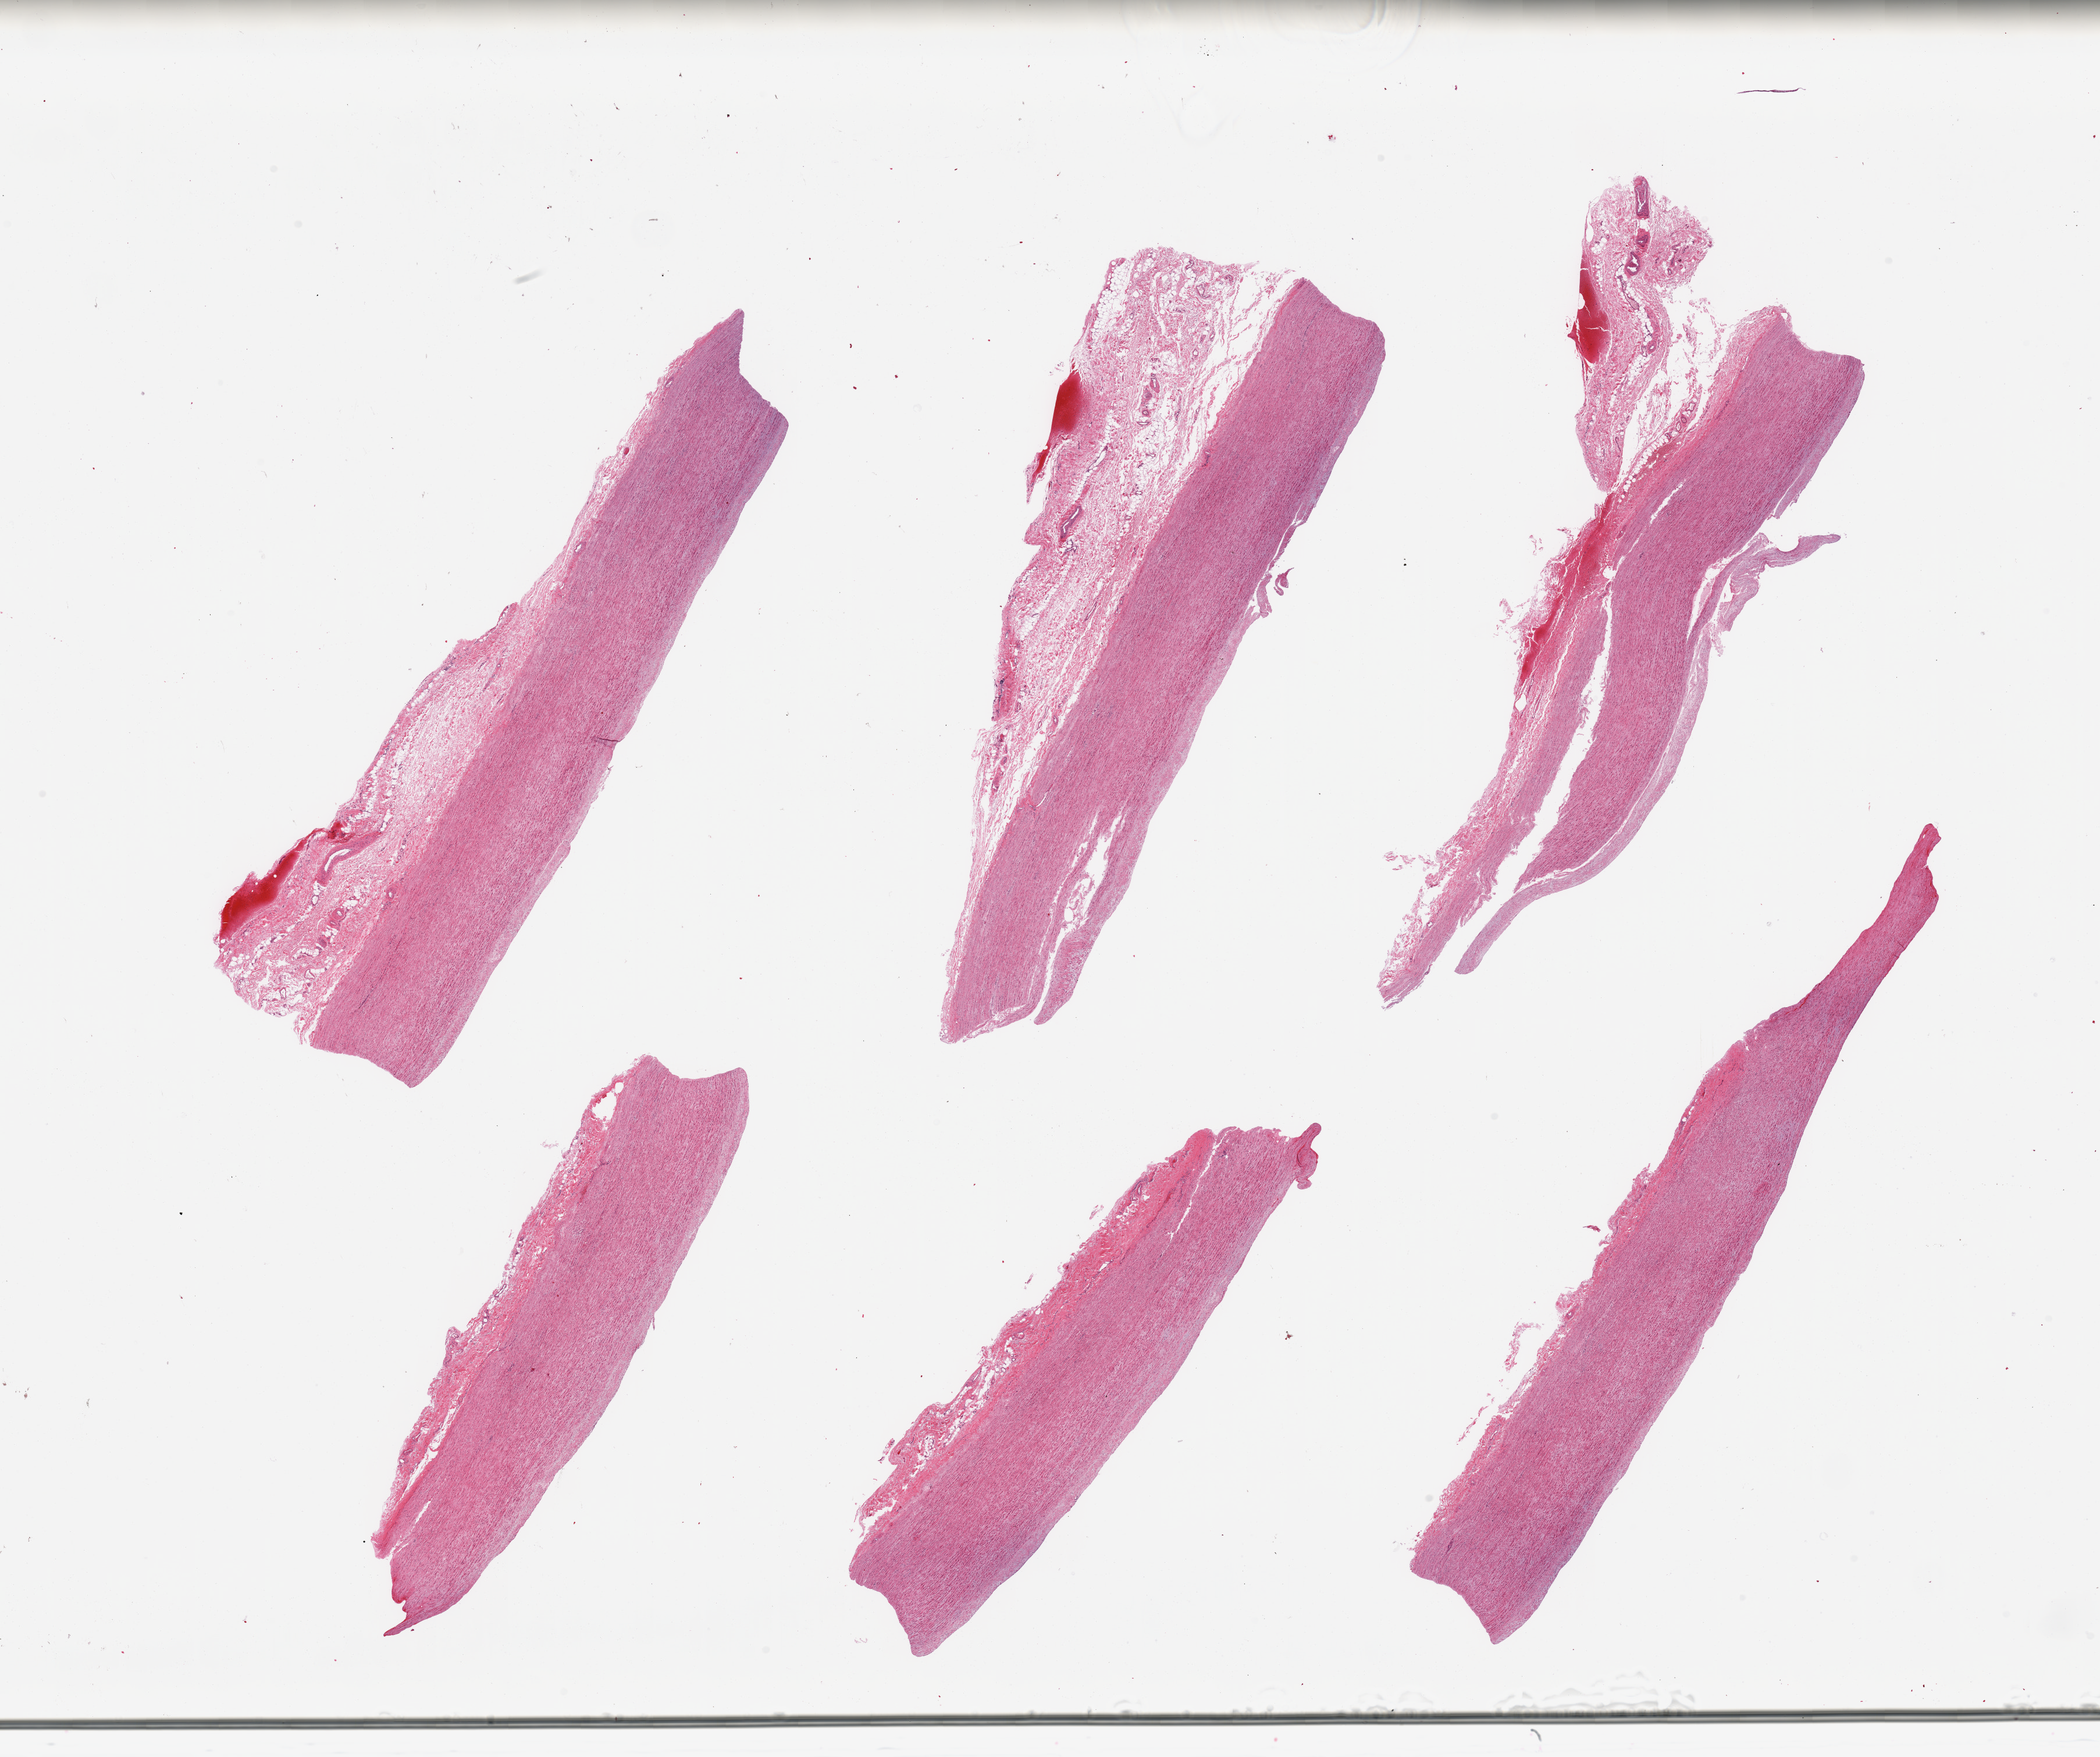
Haematoxylin and eosin whole-slide image, brightfield, whole scanned area (about 28.5 x 23.9 mm) shown as a low-resolution overview. PAXgene-fixed paraffin-embedded (PFPE) section. Target tissue: aorta. Tissue donor sample. Donor: male.
Review note (as recorded): 6 pieces, atherosis up to ~0.5mm; adherent serosal fat up to ~2mm.